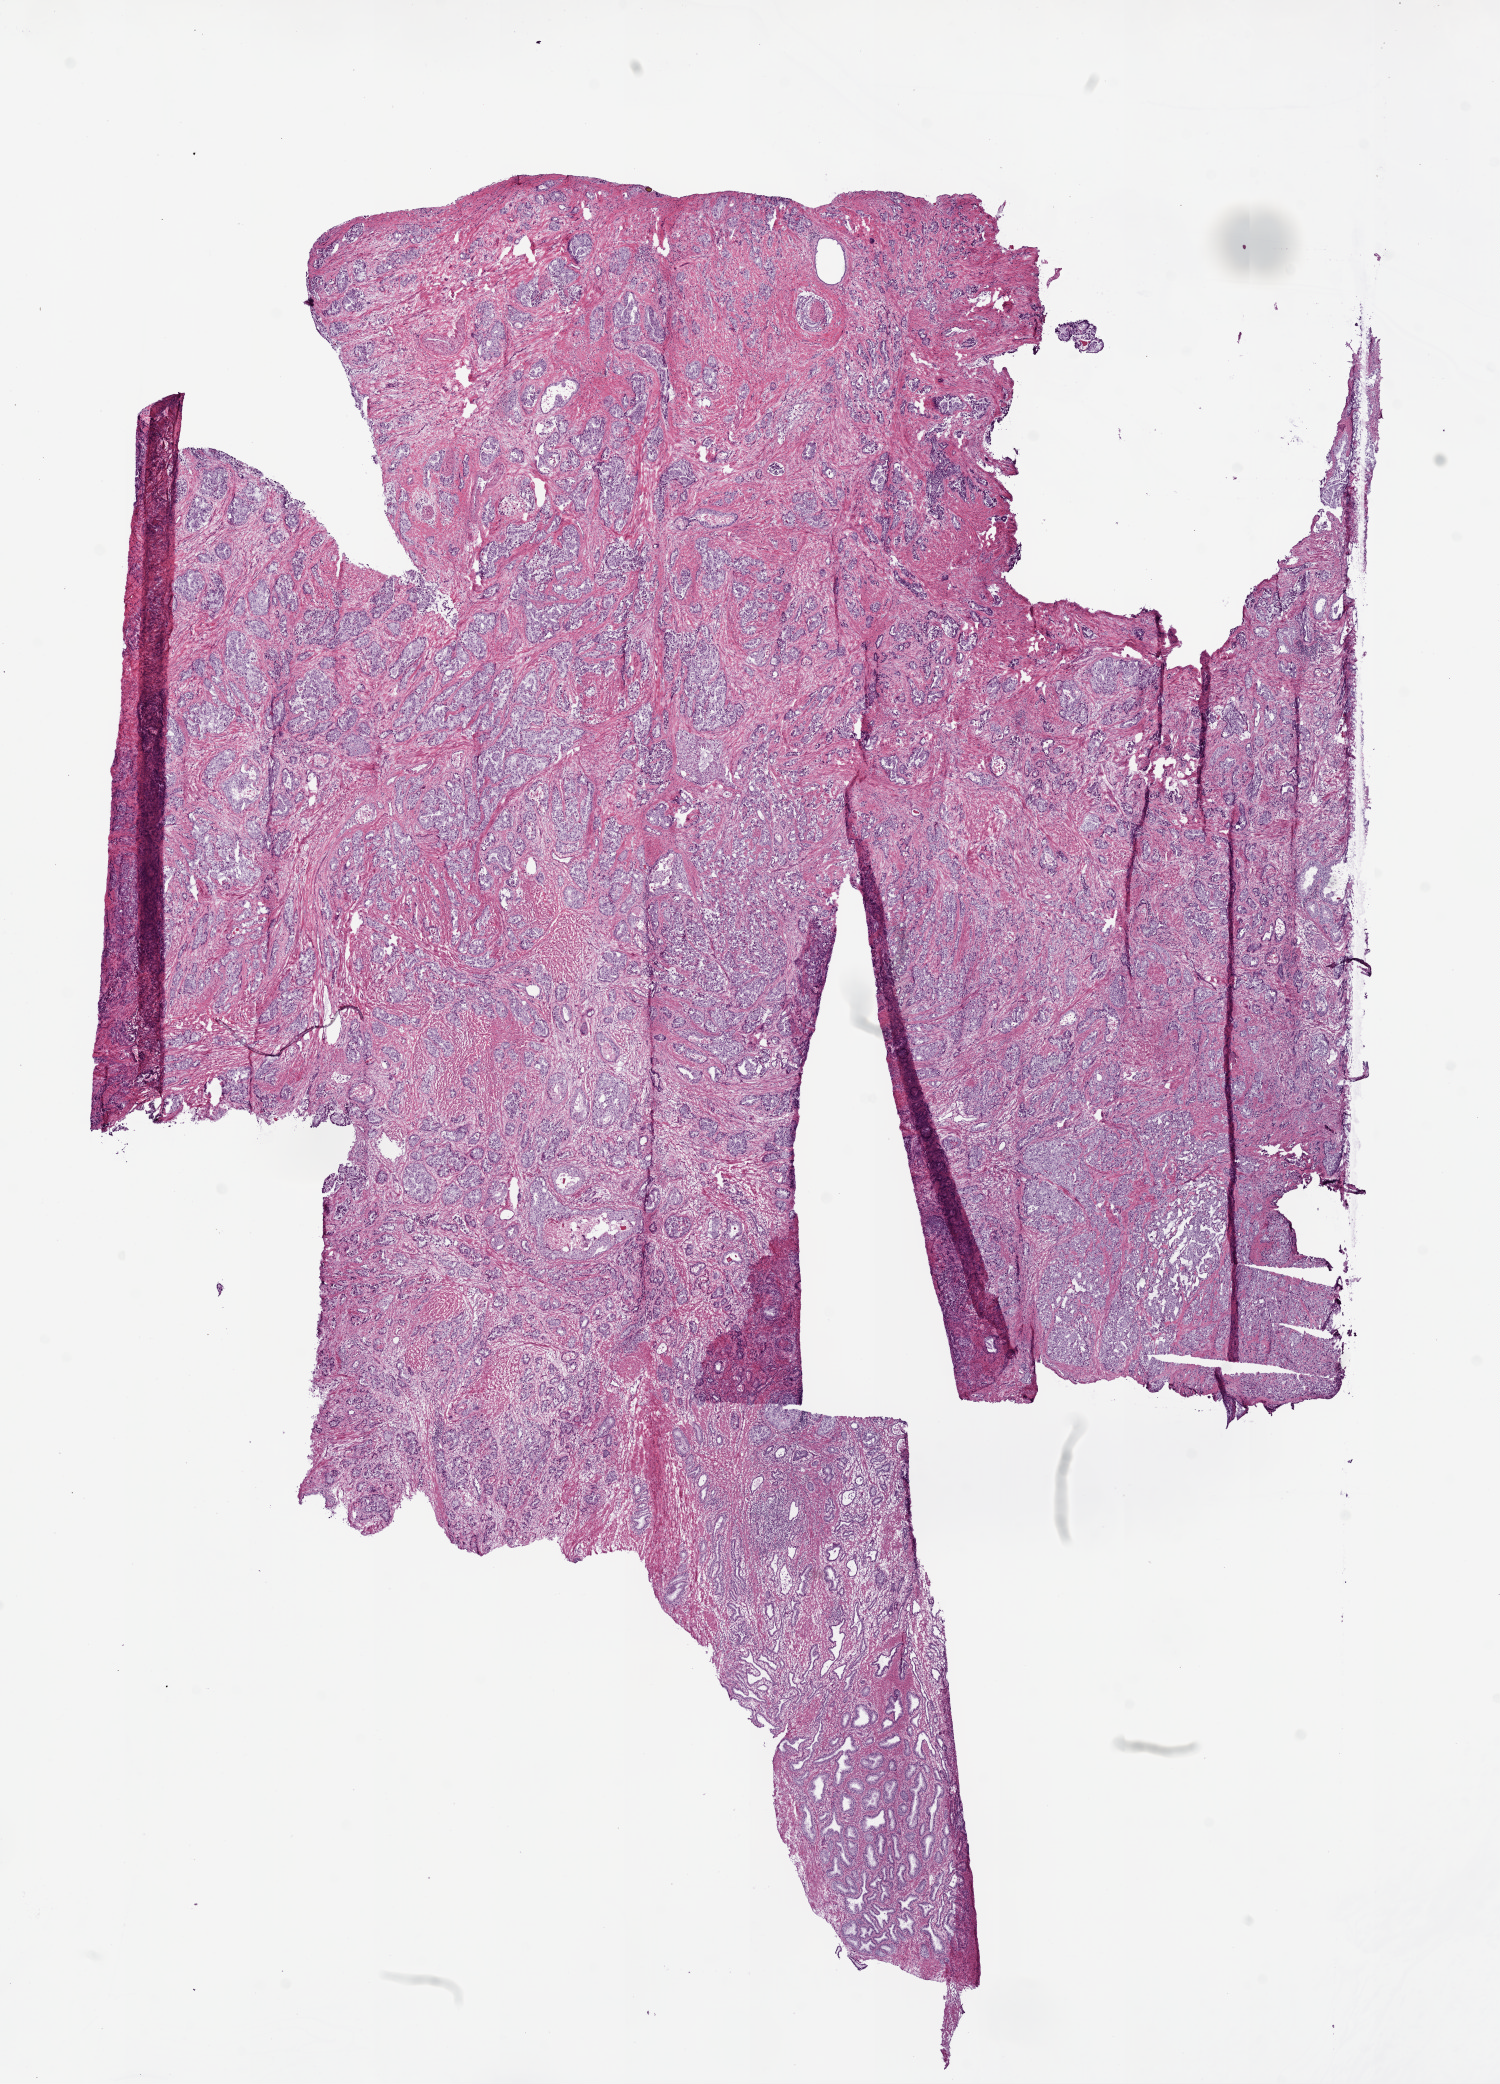
Hematoxylin and eosin (H&E) stained whole-slide image, low-resolution overview of the scanned area, about 12.0 x 16.7 mm, frozen section, primary tumour sample from the prostate. Patient: male, age at initial diagnosis 66 years. Gleason score: 9 (4+5). Pathologist review of this section (percent, as recorded): tumour cells 65%, tumour nuclei 70%, normal cells 5%, stromal cells 28%, necrosis 2%. Infiltration values recorded for this section: lymphocyte infiltration 2%, monocyte infiltration 2%, neutrophil infiltration 2%.
Laterality: bilateral. Lymph nodes positive (case pathology): 0 of 12 examined. Pathologic diagnosis: Acinar cell carcinoma (prostate gland).